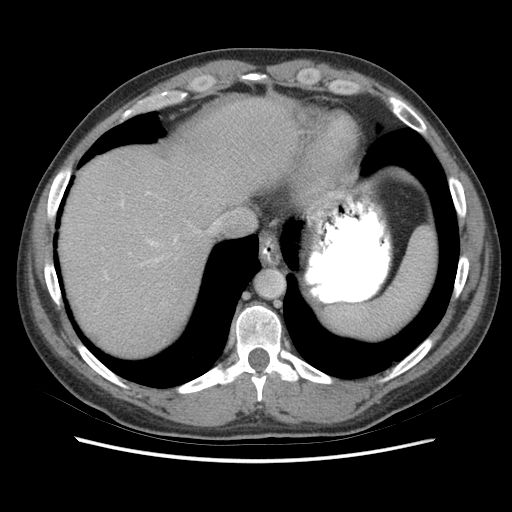
Contrast-enhanced abdominal CT (liver protocol), one axial slice. Position 61 of 73 along the scan axis. Reconstruction kernel STANDARD. 140 kVp. Soft-tissue window (W 400 / L 40 HU). 2.5 mm slice thickness. 512 × 512 image matrix, field of view 360 × 360 mm. Case-level facts recorded for this patient, not image findings: diagnosis: hepatocellular carcinoma (patient treated with transarterial chemoembolisation; whether this scan precedes or follows treatment is not stated here); TNM stage (as recorded): Stage-IIIA; Child-Pugh class: A; tumour nodularity: multinodular.
Outlined on this slice (semi-automatically segmented with operator editing):
- abdominal aorta: bounding box (x1, y1, x2, y2) in pixels: (256, 270, 284, 297)
- liver parenchyma outside the tumour (the mass and vessels are separate outlines, so this box may not span the whole liver): (60, 98, 300, 356)
- liver vessels: (105, 192, 177, 279)